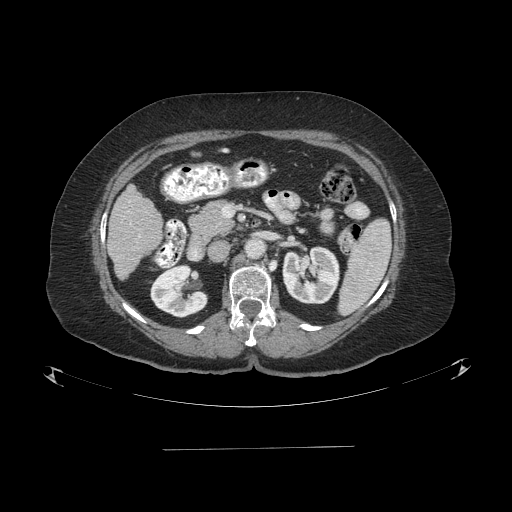
Contrast-enhanced abdominal CT (liver protocol), one axial slice; slice 34 of 103 in the series (ordered by position); reconstruction kernel STANDARD; 120 kVp; one of 2 acquisitions stored at this slice position; soft-tissue window (W 400 / L 40 HU); 512 × 512 image matrix, field of view 500 × 500 mm. From the clinical record (not read from this slice): diagnosis: hepatocellular carcinoma (patient treated with transarterial chemoembolisation; whether this scan precedes or follows treatment is not stated here); TNM stage (as recorded): Stage-IIIA; Child-Pugh class: A; tumour nodularity: multinodular.
Annotated regions visible in this slice (semi-automatic segmentation, software-assisted and operator-edited):
- liver parenchyma outside the tumour (the mass and vessels are separate outlines, so this box may not span the whole liver): bounding box <108,184,162,278> (left, top, right, bottom; pixels)